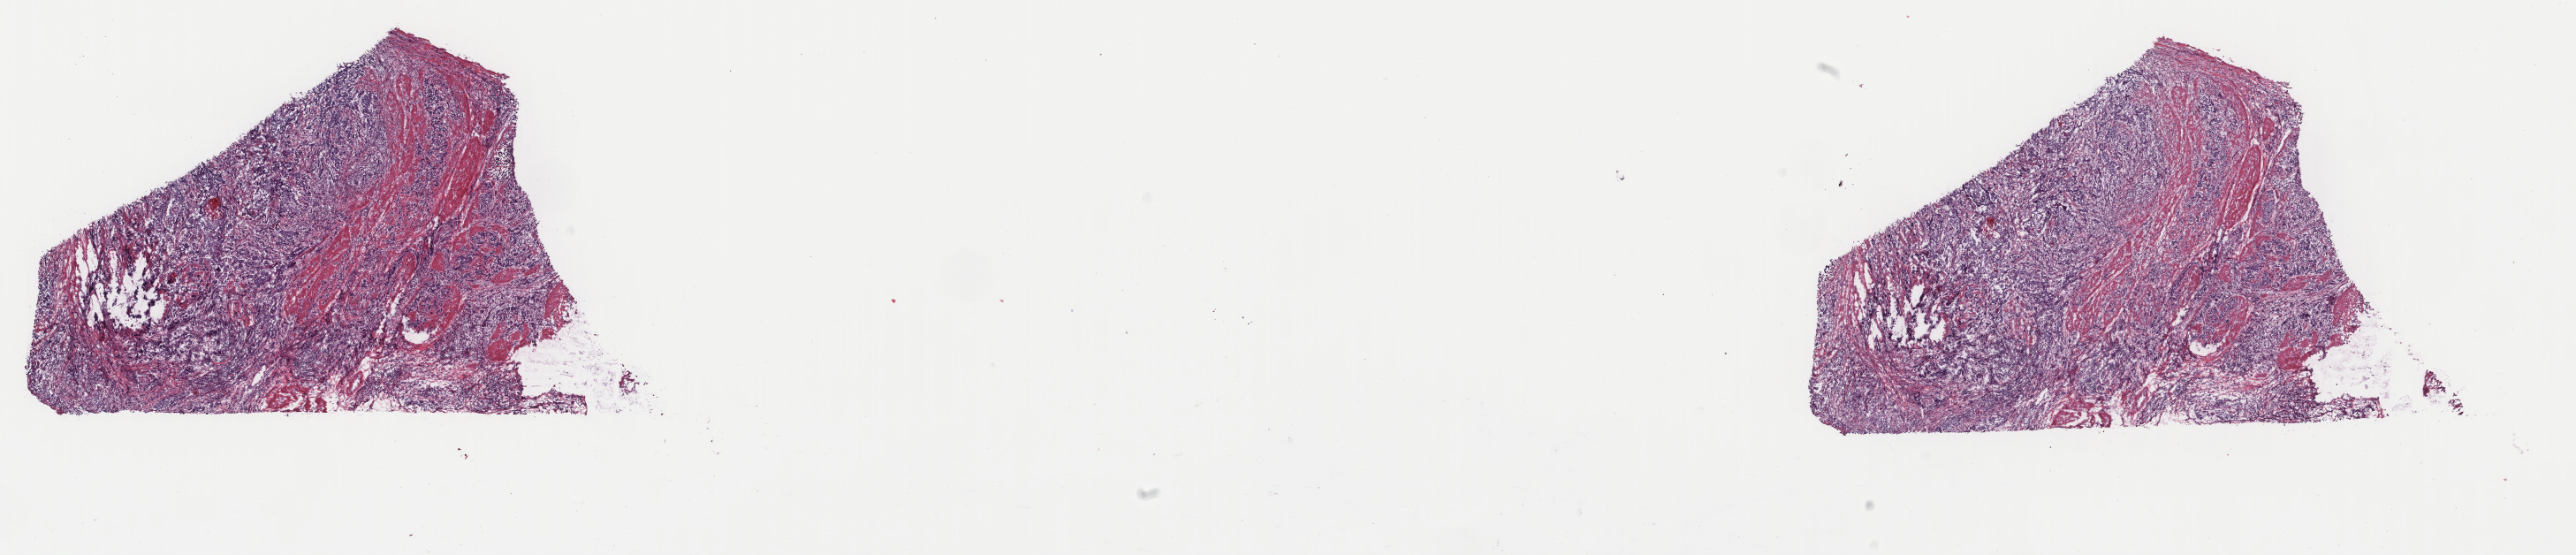
Hematoxylin and eosin (H&E) stained whole-slide image — a low-resolution overview of the entire scanned area, about 23.1 x 5.0 mm. Frozen section. Sample: primary tumour, esophagus. Patient: male, age at initial diagnosis 73 years. Histologic grade: G3 (poorly differentiated). Pathologist review of this section (percent, as recorded): tumour cells 100%, tumour nuclei 85%, normal cells 0%, stromal cells 0%, necrosis 0%. Inflammatory infiltration, as recorded: lymphocyte infiltration 0%, monocyte infiltration 0%, neutrophil infiltration 0%.
* AJCC pathologic stage: III
* histologic diagnosis: Squamous cell carcinoma, NOS (middle third of esophagus)
* lymph nodes positive (case pathology): 2 of 2 examined